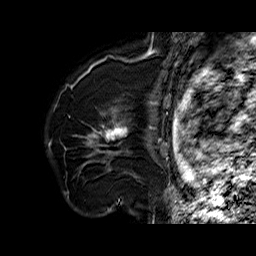
Breast MRI (dynamic contrast-enhanced), one sagittal slice; slice 47 of 60 in the series (ordered by position); dynamic contrast-enhanced series, time point 2 of 6 at this slice position (early post-contrast); 1.5 T; TE 6.4 ms, TR 32.7 ms; 4 mm slice thickness; 256 × 256 image matrix, field of view 200 × 200 mm. Female patient. From the clinical record (not read from this slice): setting: breast cancer imaged before/during neoadjuvant chemotherapy; receptor status: HR-positive, HER2-negative.
Structures marked on this image (semi-automatically segmented with operator editing):
- analysis volume of interest (the breast-tissue region the enhancement analysis was run in; not a lesion): bounding box [x1, y1, x2, y2] px = [79, 110, 138, 179]
- tumour enhancement mask (voxels above the 100 % enhancement threshold inside the analysis volume of interest): [89, 122, 128, 162]